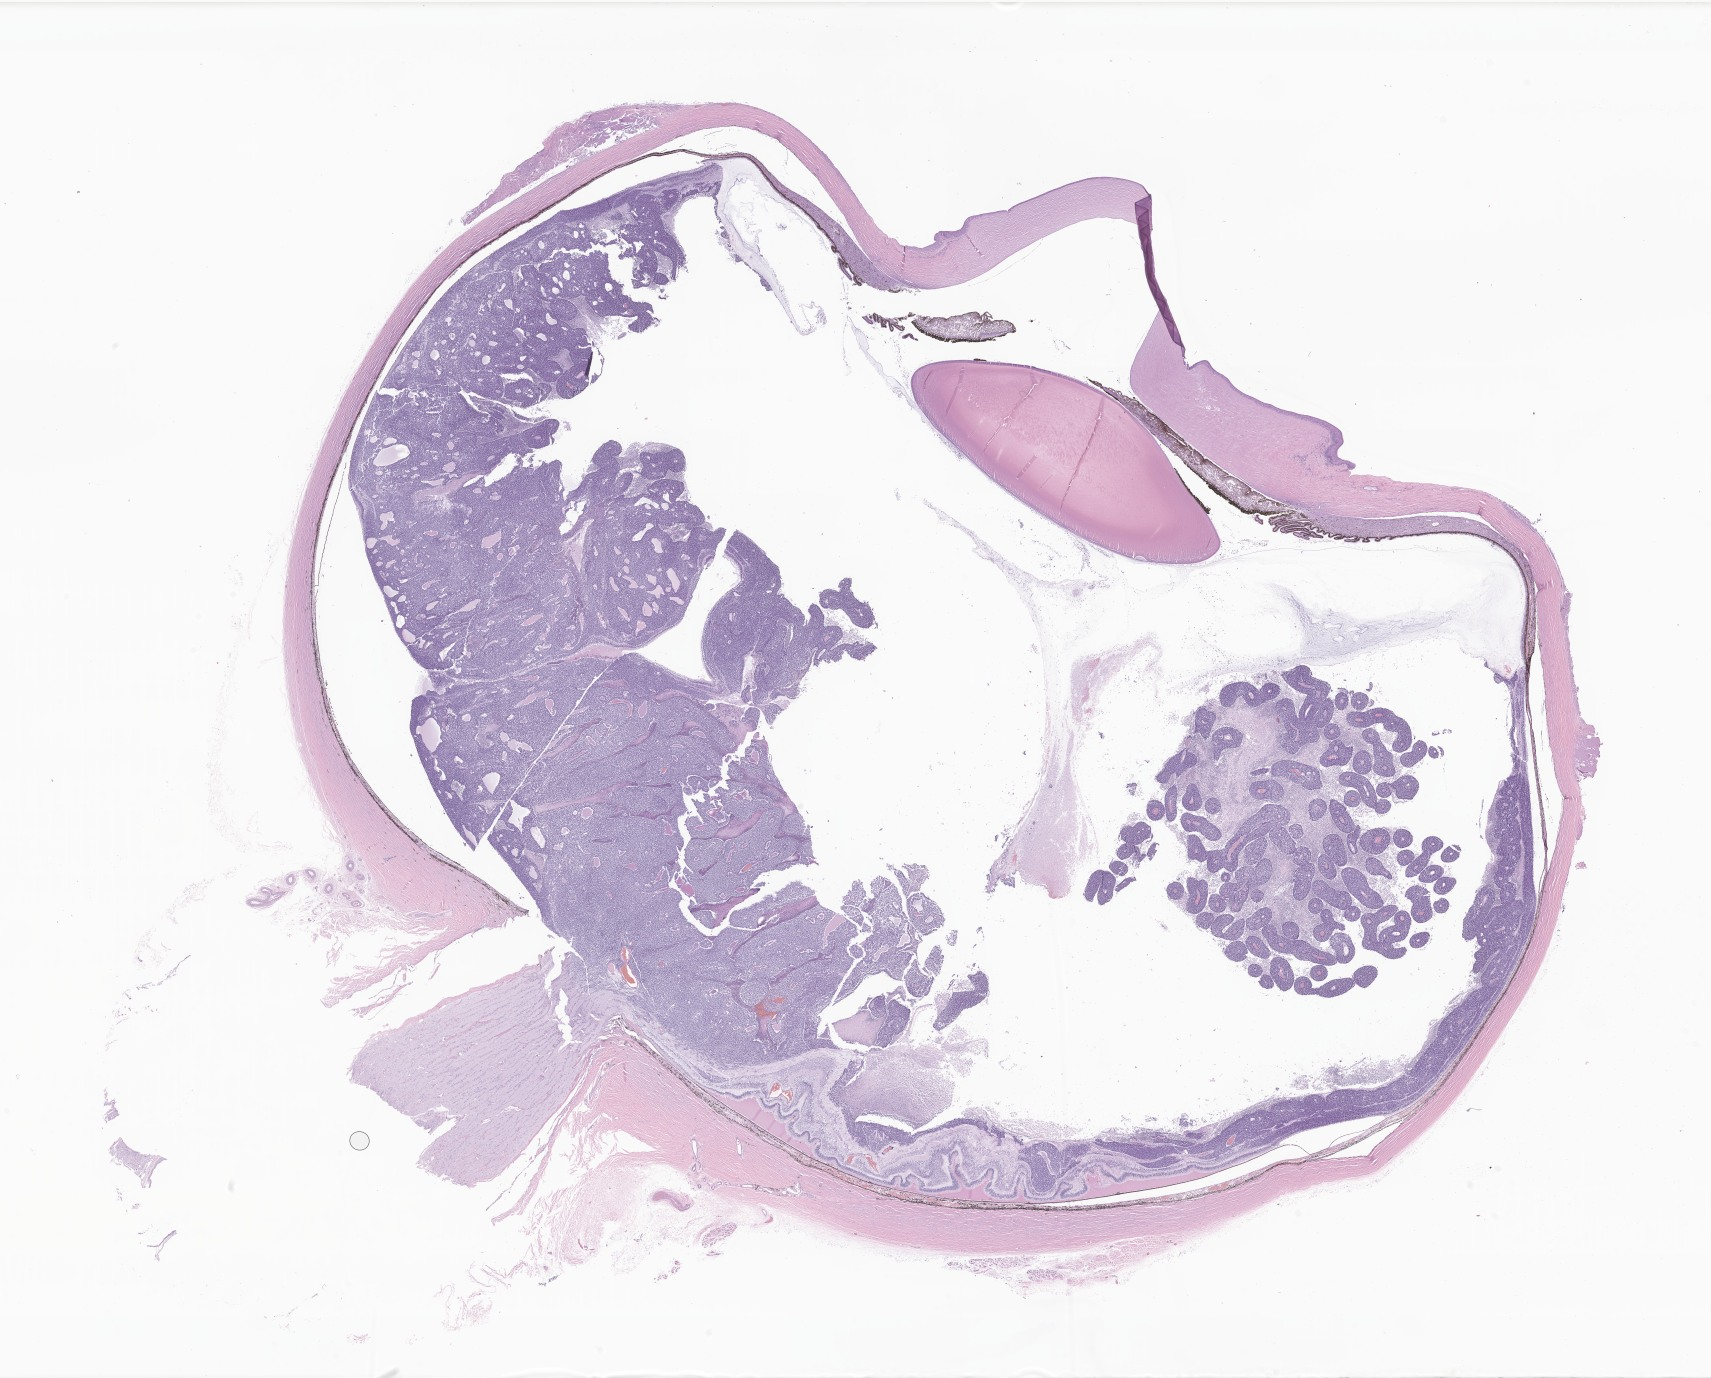
Haematoxylin and eosin whole-slide image of tumor tissue from the retina — whole scanned area (about 28.9 x 23.2 mm) shown as a low-resolution overview. Formalin-fixed, paraffin-embedded (FFPE) tissue. Female patient, age 45 months (3 years 9 months).
Diagnosis: Retinoblastoma, NOS.